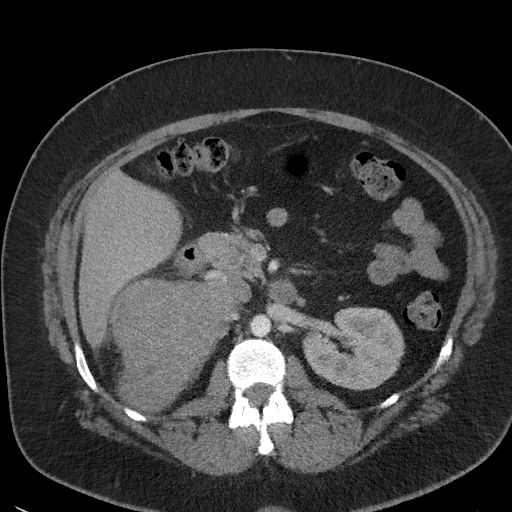
Contrast-enhanced abdominal CT, one axial slice; position 24 of 56 along the scan axis; intravenous contrast given; soft-tissue window (W 400 / L 40 HU); 5 mm slice thickness; 512 × 512 image matrix, field of view 373 × 373 mm. Female patient, age 35 years. Case-level facts recorded for this patient, not image findings: diagnosis: adrenocortical carcinoma; tumour side: right adrenal; tumour size at pathology: 15 cm; Ki-67 index: 40 %; stage (as recorded): 2.
Outlined on this slice (semi-automatically segmented with operator editing):
- mass: bounding box <115,281,230,408> (left, top, right, bottom; pixels)